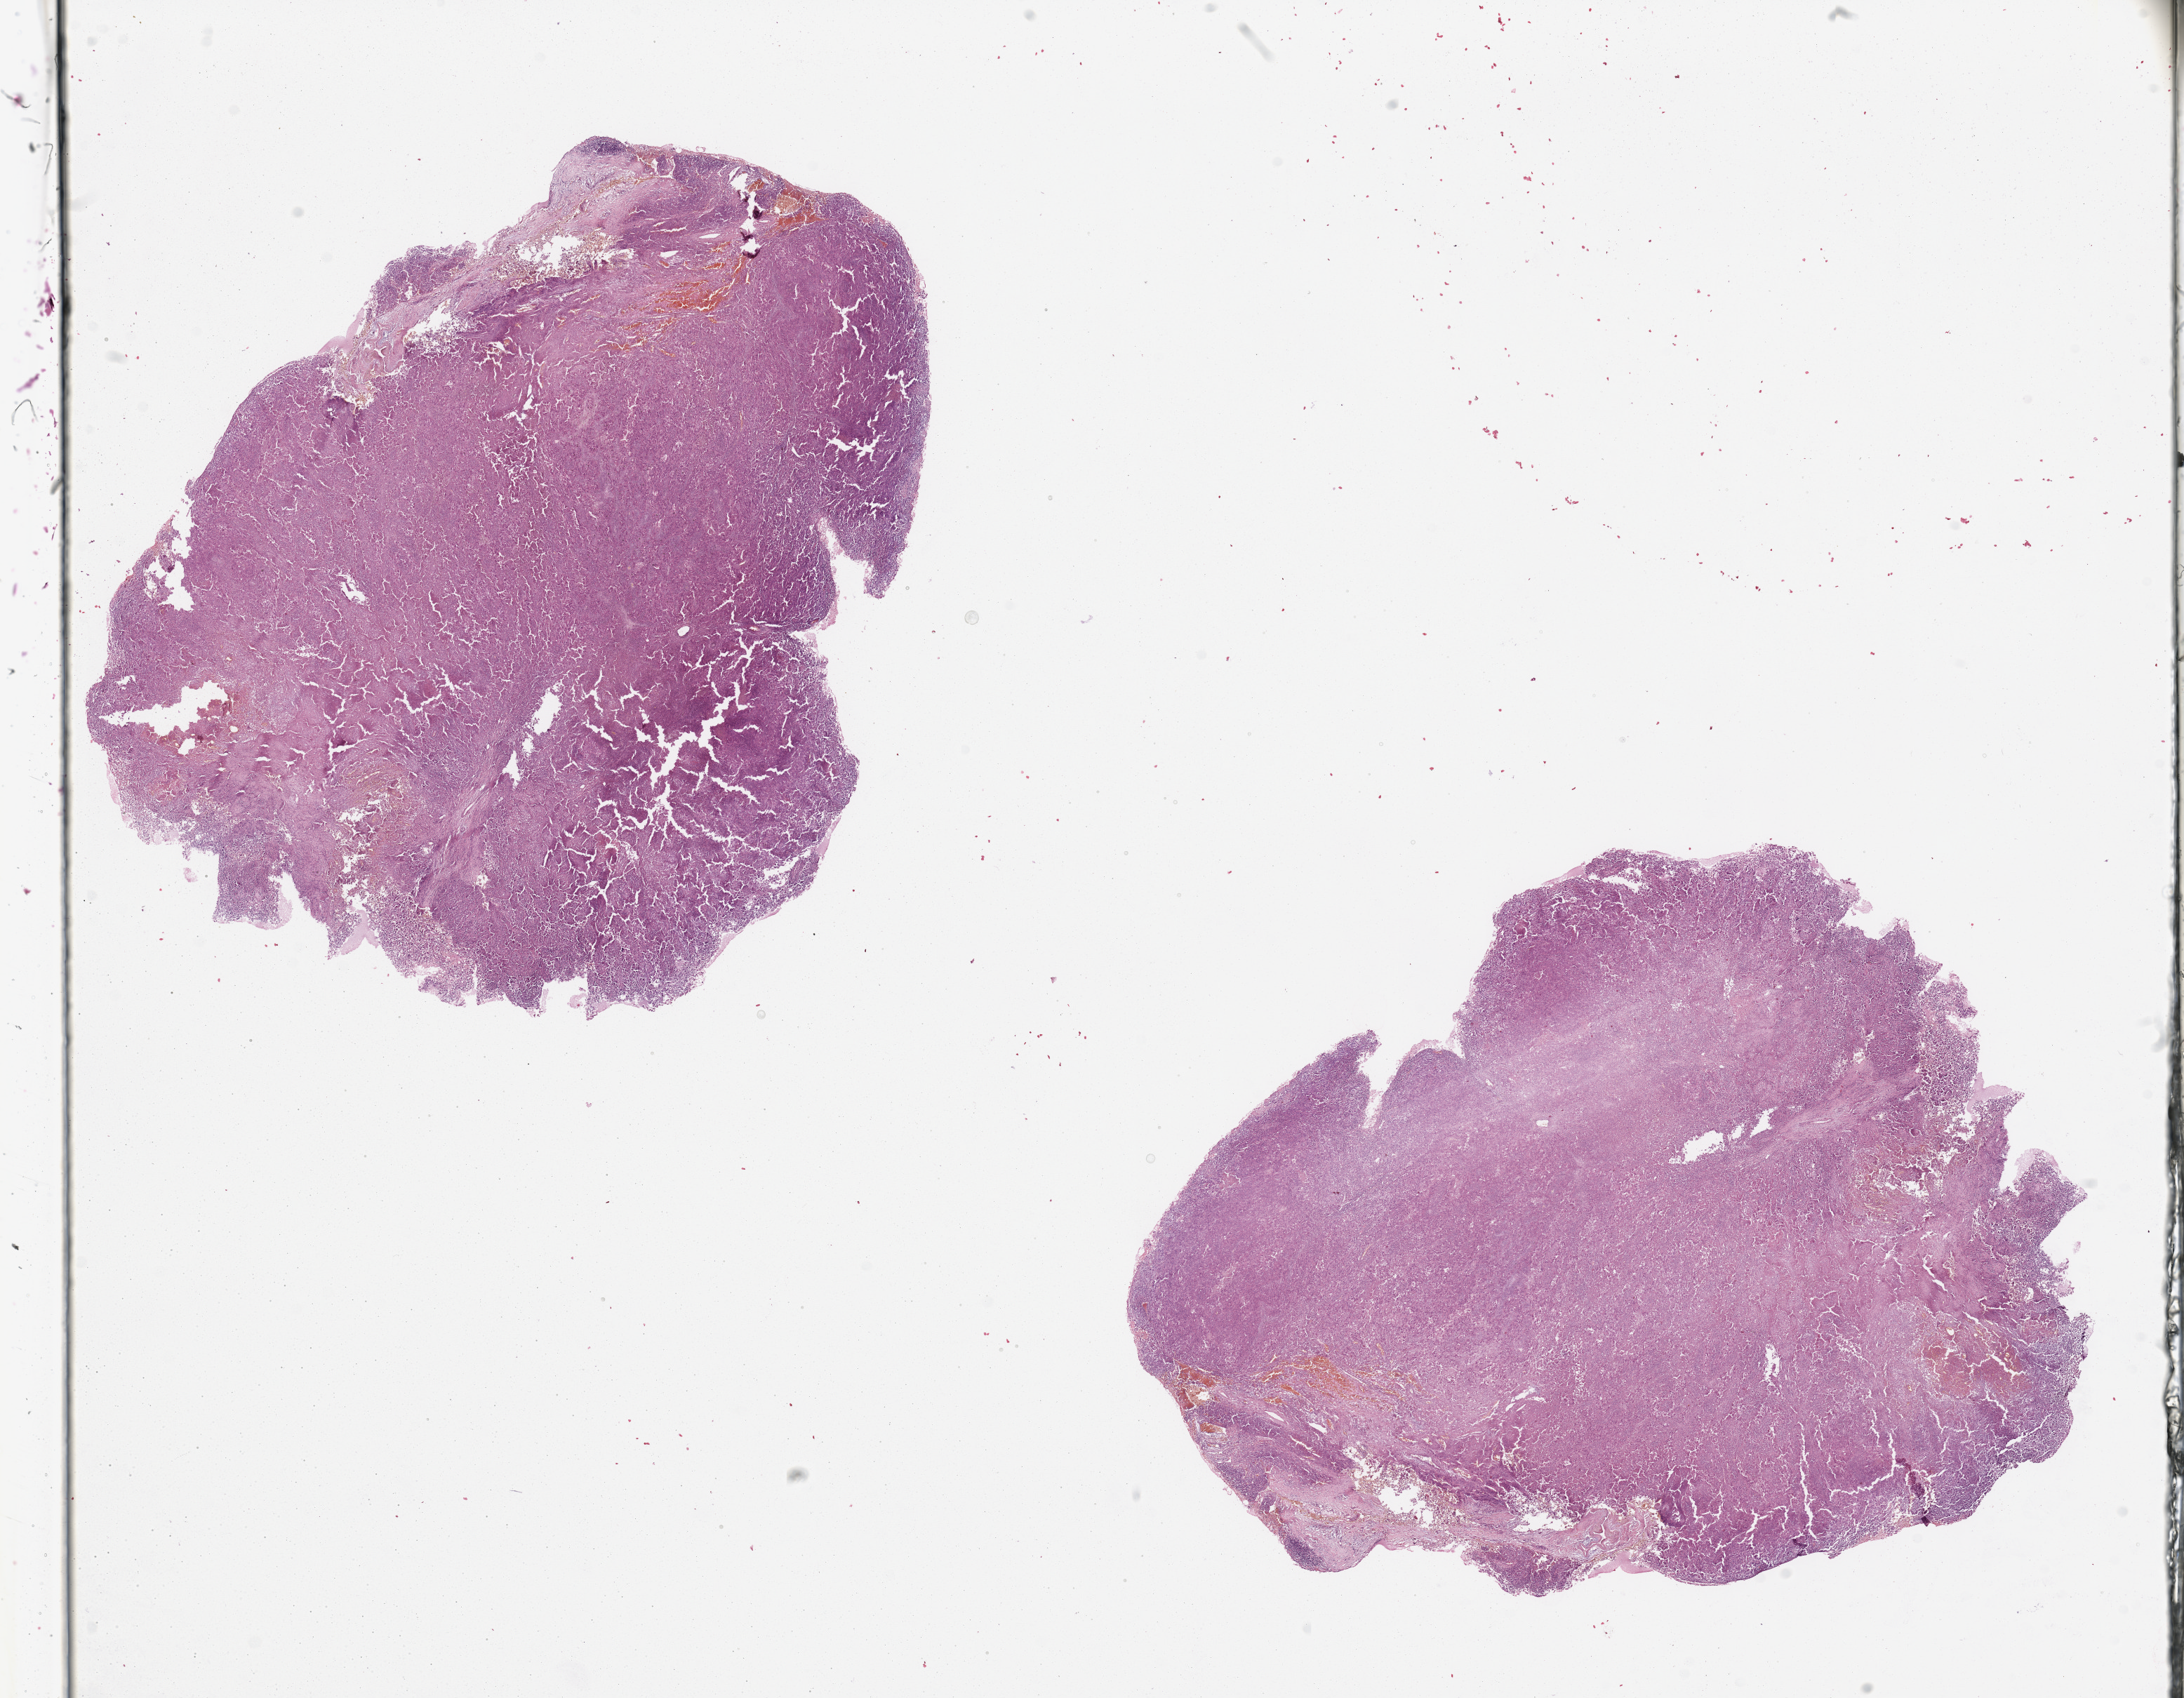
H&E-stained whole-slide image — whole scanned area (about 24.6 x 19.1 mm) shown as a low-resolution overview, melanoma tumour tissue; sampled site not recorded. Patient: male, age 62 years.
Primary tumour site (as recorded): trunk. Diagnosis: Malignant melanoma, NOS. AJCC pathologic stage: IIB.